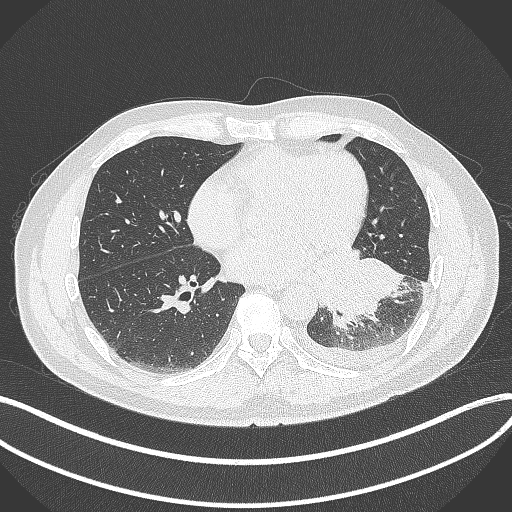
Chest CT, one axial slice. Position 147 of 342 along the scan axis. 120 kVp. Lung window (W 1500 / L -600 HU). 1 mm slice thickness. 512 × 512 image matrix, field of view 400 × 400 mm. Male patient, age 58 years. From the clinical record (not read from this slice): clinical TNM (as recorded): T3 N1 M1b.
Structures marked on this image (bounding box drawn by a radiologist):
- lung tumour (recorded histology: small cell carcinoma): bounding box [x1, y1, x2, y2] px = [314, 246, 408, 329]